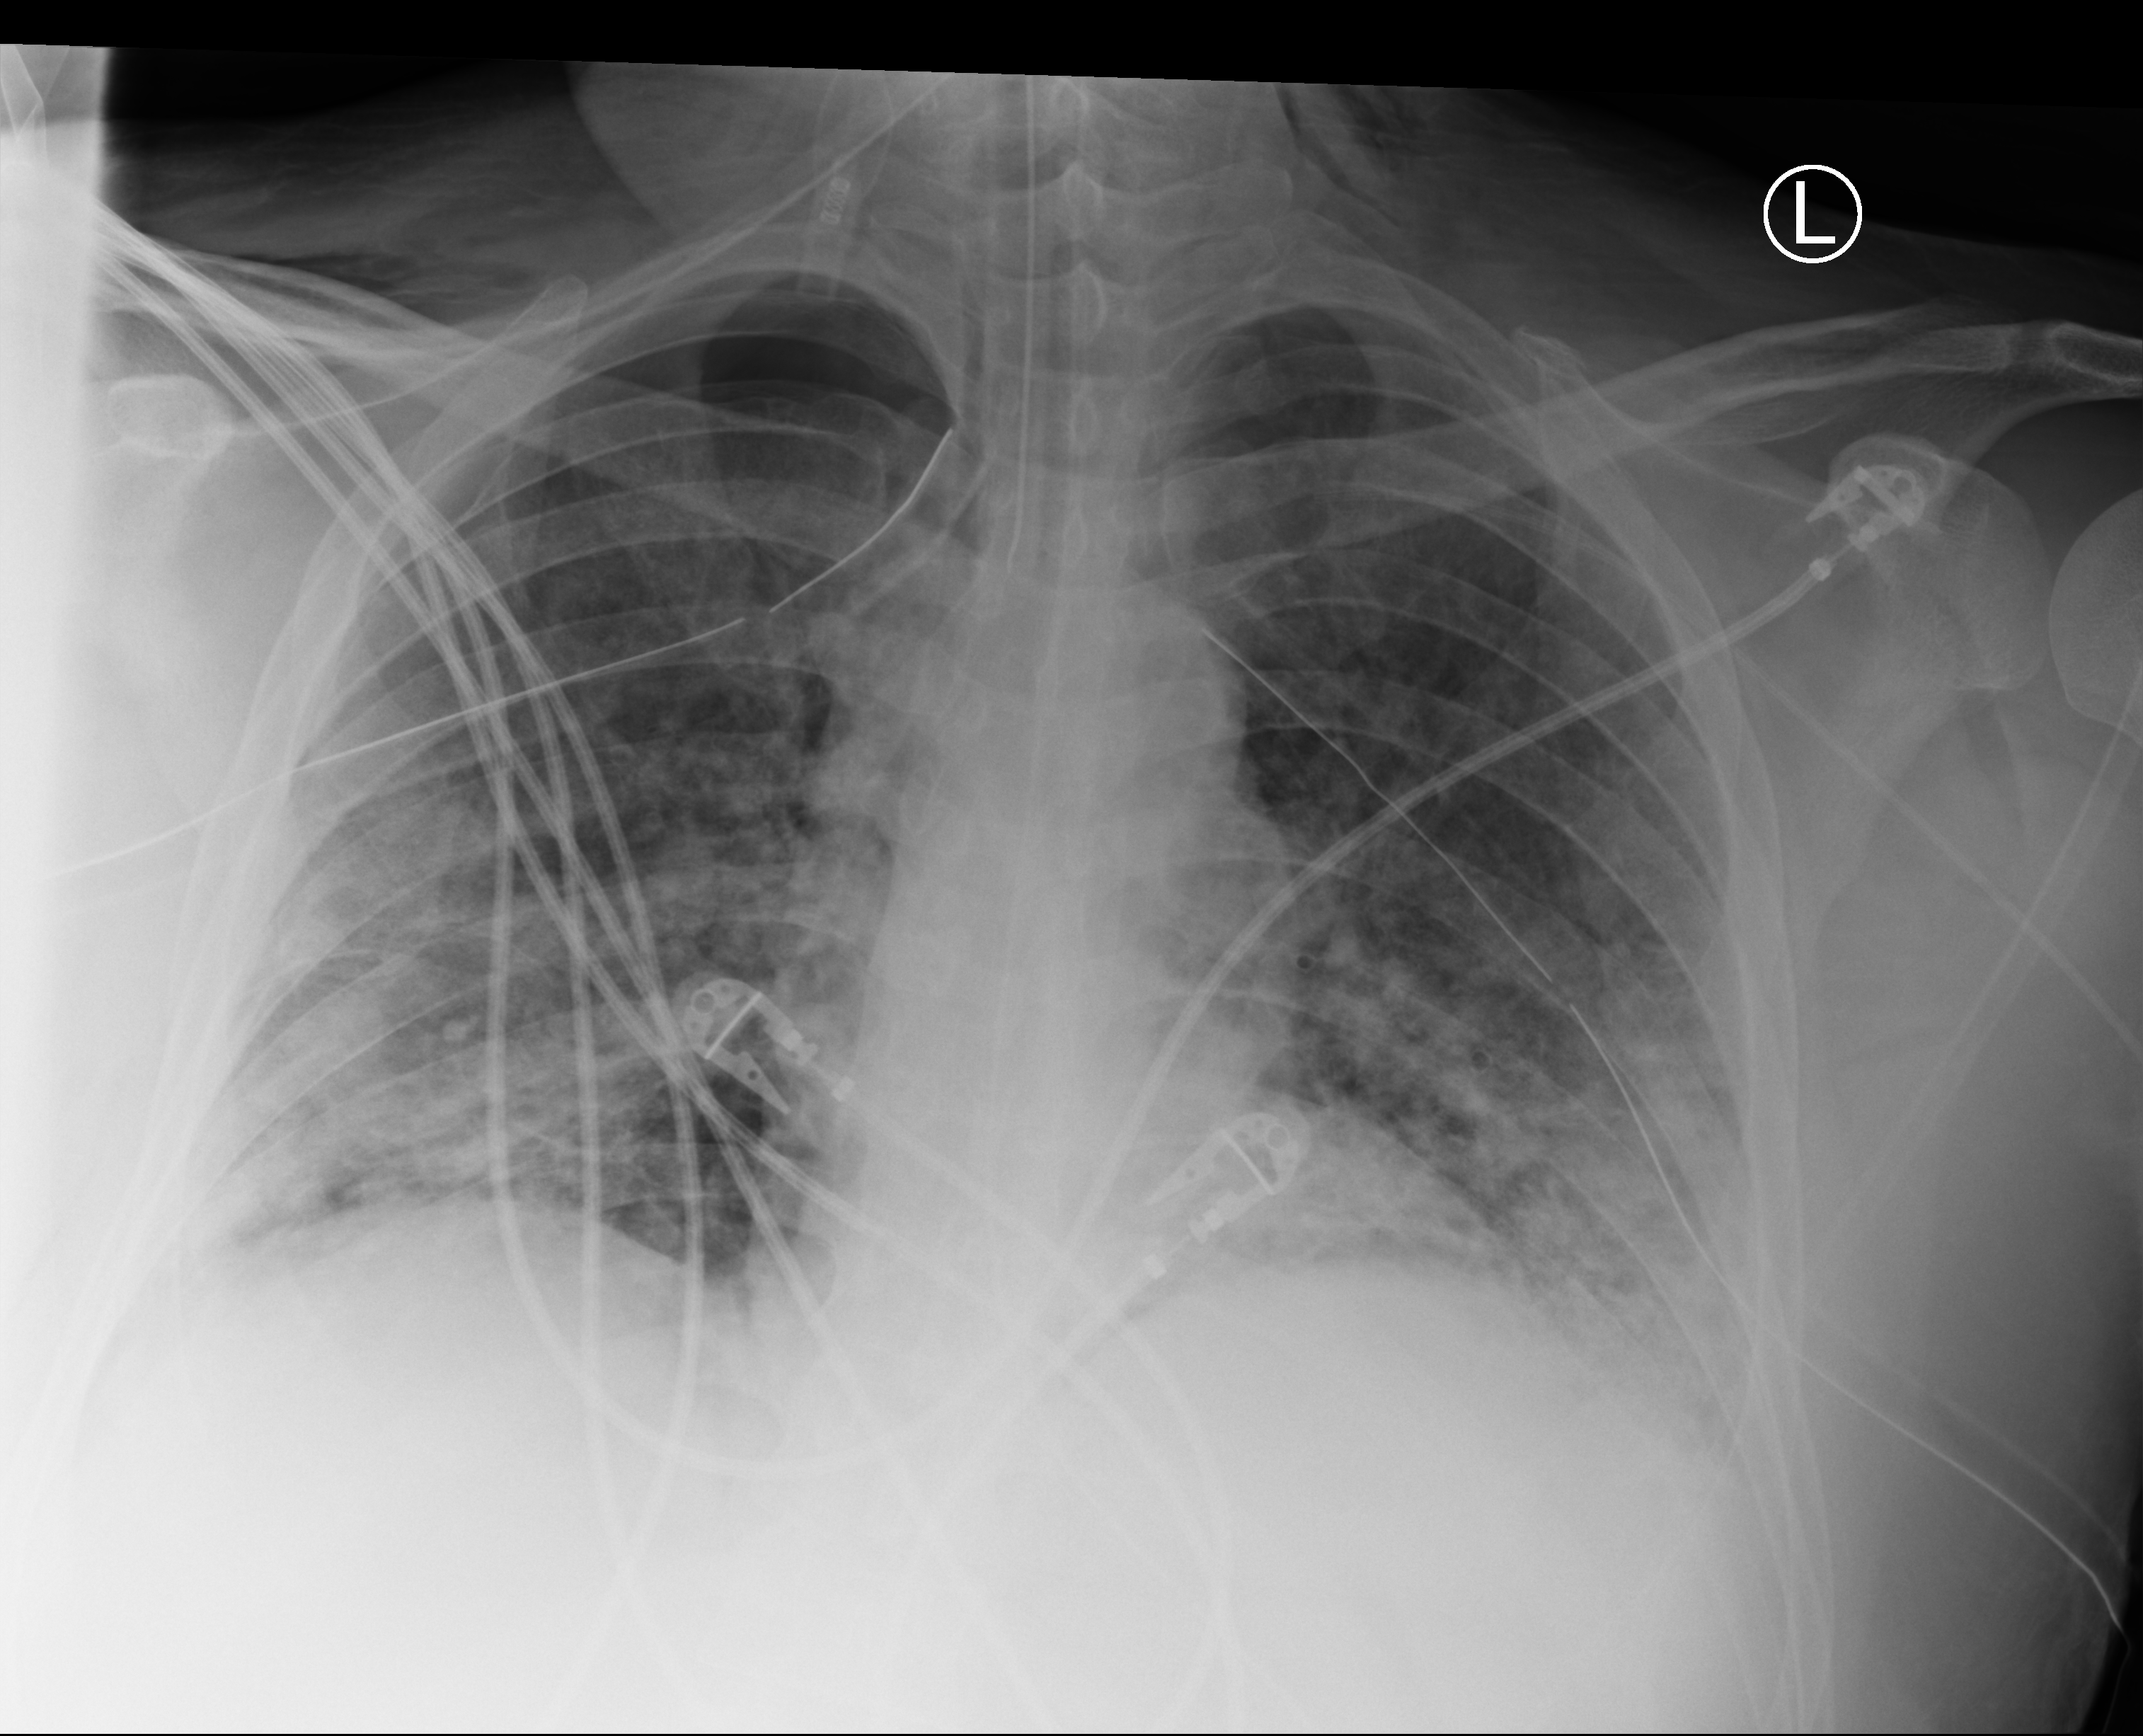
Bedside chest radiograph (computed radiography), anteroposterior (AP) projection. Patient hospitalised with COVID-19; male, aged 18–59 years.
Hospital-stay facts (about this admission, not read from this image; timing relative to this image not recorded): smoking status (admission record): never; length of hospital stay: 63 days; mechanically ventilated during this hospital stay: yes.